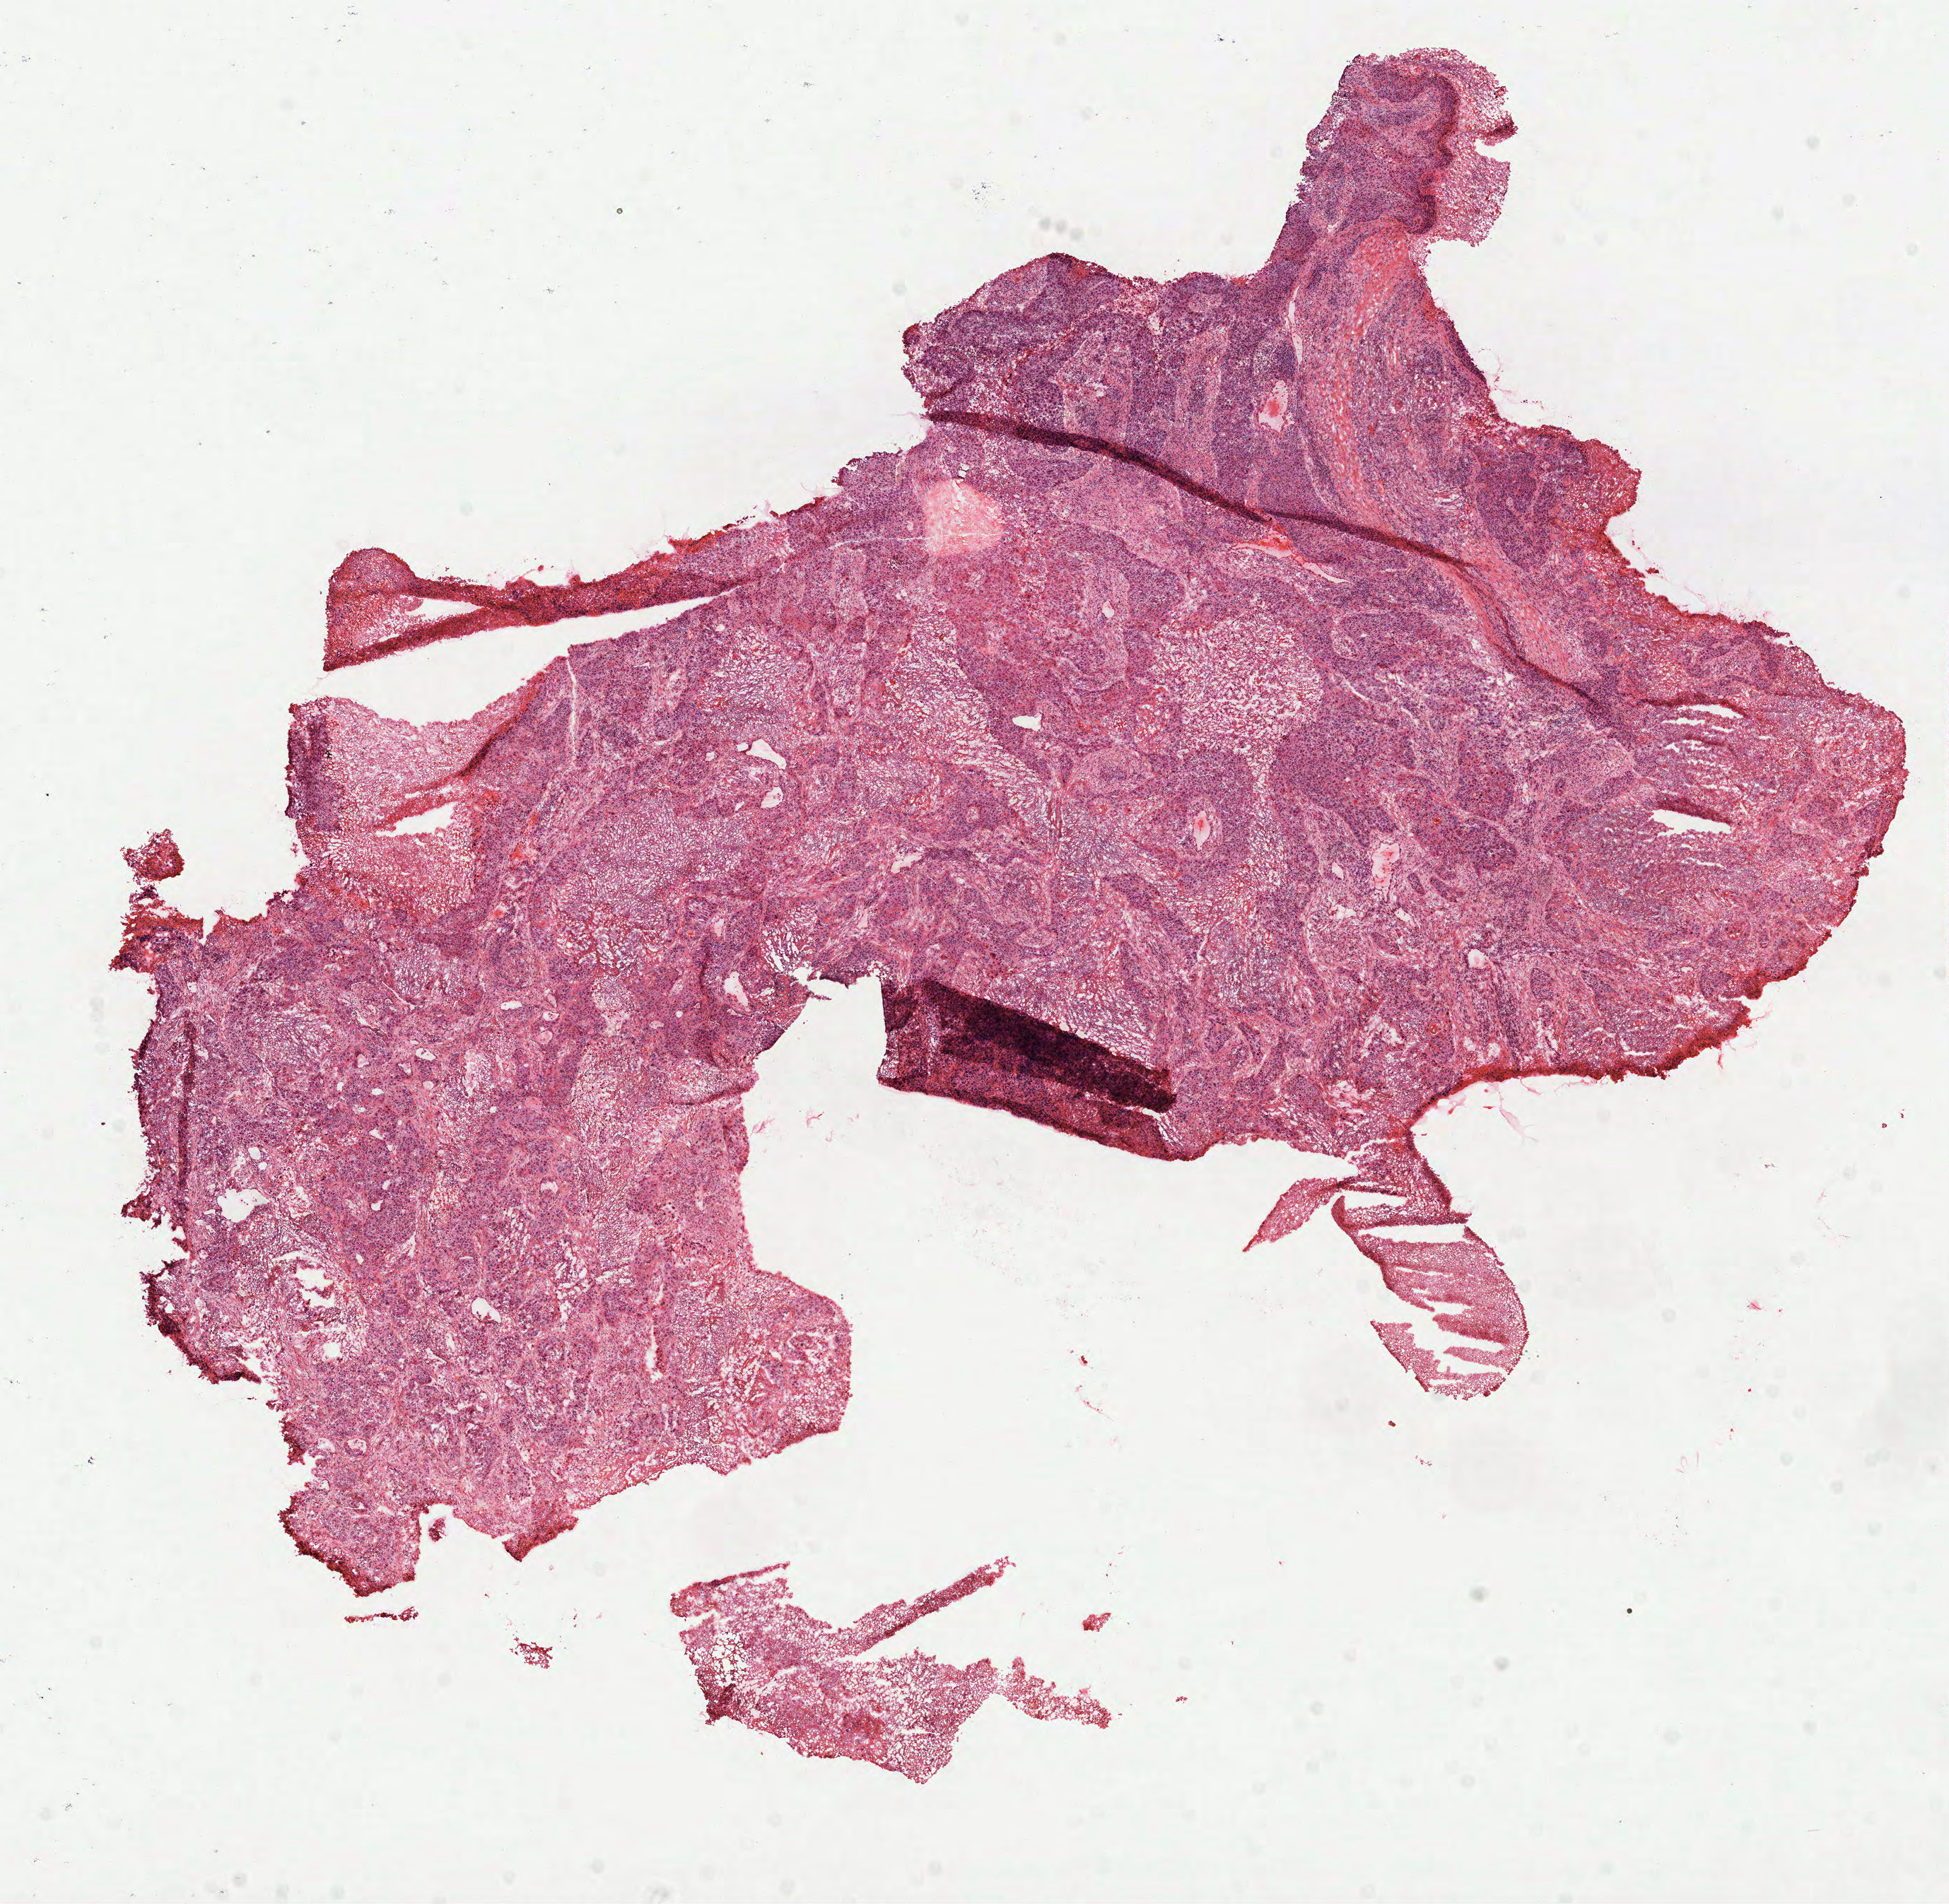
Digitized Hematoxylin and eosin (H&E) stained tissue section (whole slide), a low-resolution overview of the entire scanned area, about 11.1 x 10.9 mm; formalin-fixed paraffin-embedded (FFPE) diagnostic section; lung, primary tumour sample. Male, age 67 years at initial diagnosis.
Diagnosis: Squamous cell carcinoma, NOS (upper lobe, lung). AJCC pathologic stage: IB.